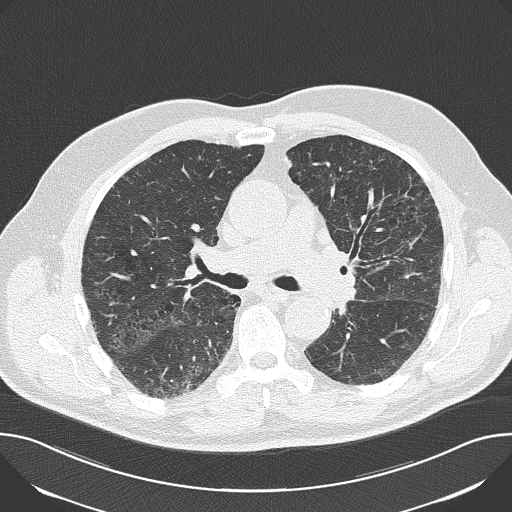
Low-dose screening chest CT, axial slice; baseline screening round; lung window (W 1500 / L -600 HU); 2 mm slice thickness; slice 71 of 163 in the series; 512 × 512 image matrix. Male, age 69 years at enrolment. Current smoker at enrolment.
Expert reader's lesion annotation, bounding box <154,362,205,406> (left, top, right, bottom; pixels). No non-calcified nodule or mass ≥4 mm was recorded by the screening reader at this exam. Official screen result: negative screen, significant abnormalities not suspicious for lung cancer. Participant outcome: lung cancer diagnosed 658 days after this screen (after the second annual screen) — squamous cell carcinoma, NOS, right lower lobe, moderately differentiated (G2), stage IA (AJCC 6th edition), 25 mm at pathology.